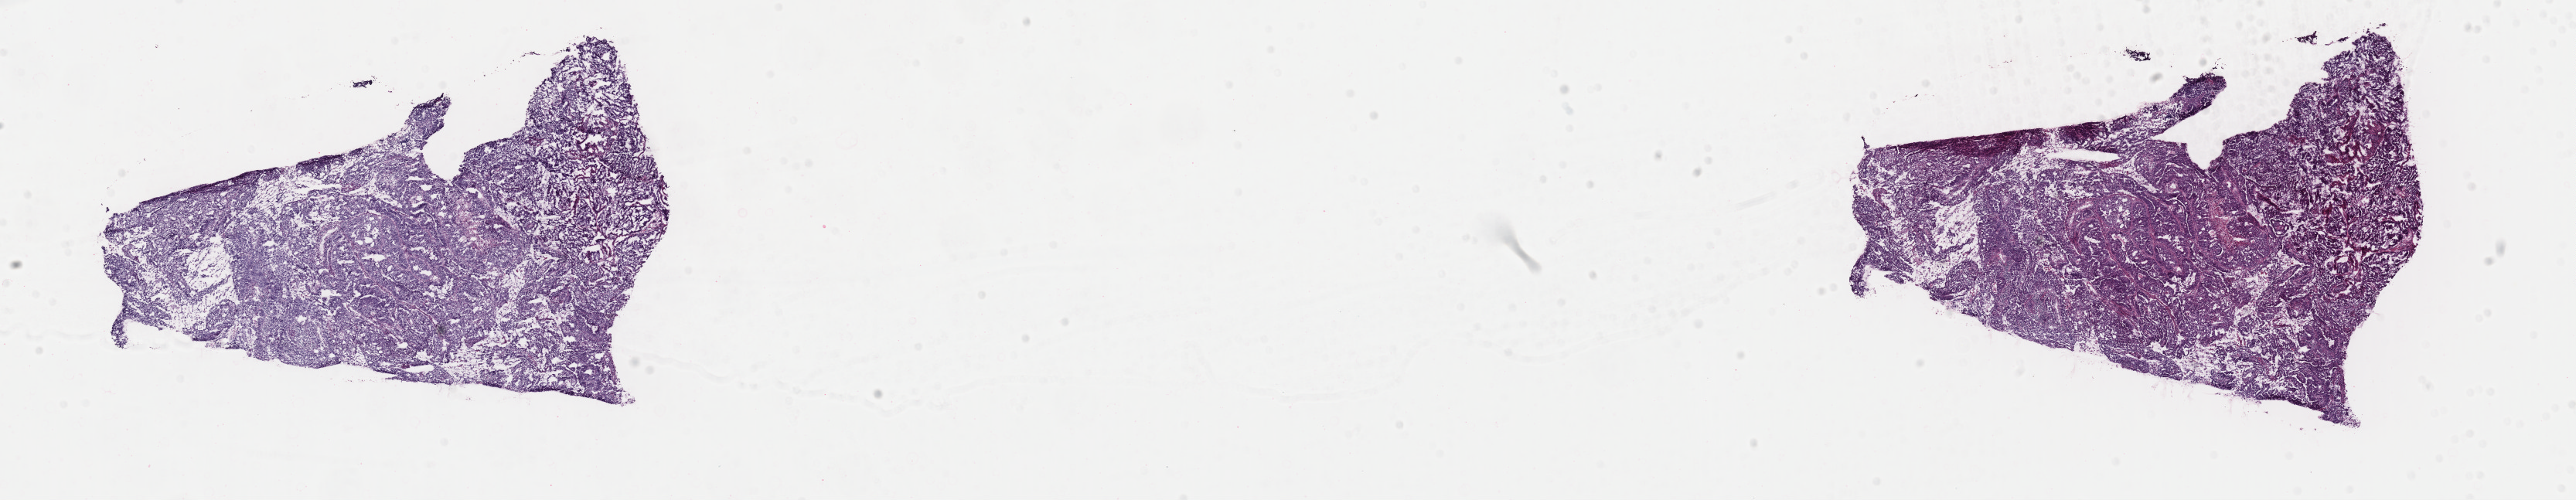
Whole-slide histology image, Hematoxylin and eosin (H&E) stained — low-resolution overview of the scanned area, about 26.3 x 5.1 mm, frozen section from the top of the tissue portion, primary tumour sample from the uterus. Patient: female, age at initial diagnosis 71 years. Histologic grade: G3 (poorly differentiated). Slide review estimates, as recorded: tumour cells 89%, tumour nuclei 90%, normal cells 0%, stromal cells 6%, necrosis 5%. Infiltration values recorded for this section: lymphocyte infiltration 6%, monocyte infiltration 0%, neutrophil infiltration 0%.
- FIGO stage: IVB
- diagnosis: Serous cystadenocarcinoma, NOS (endometrium)